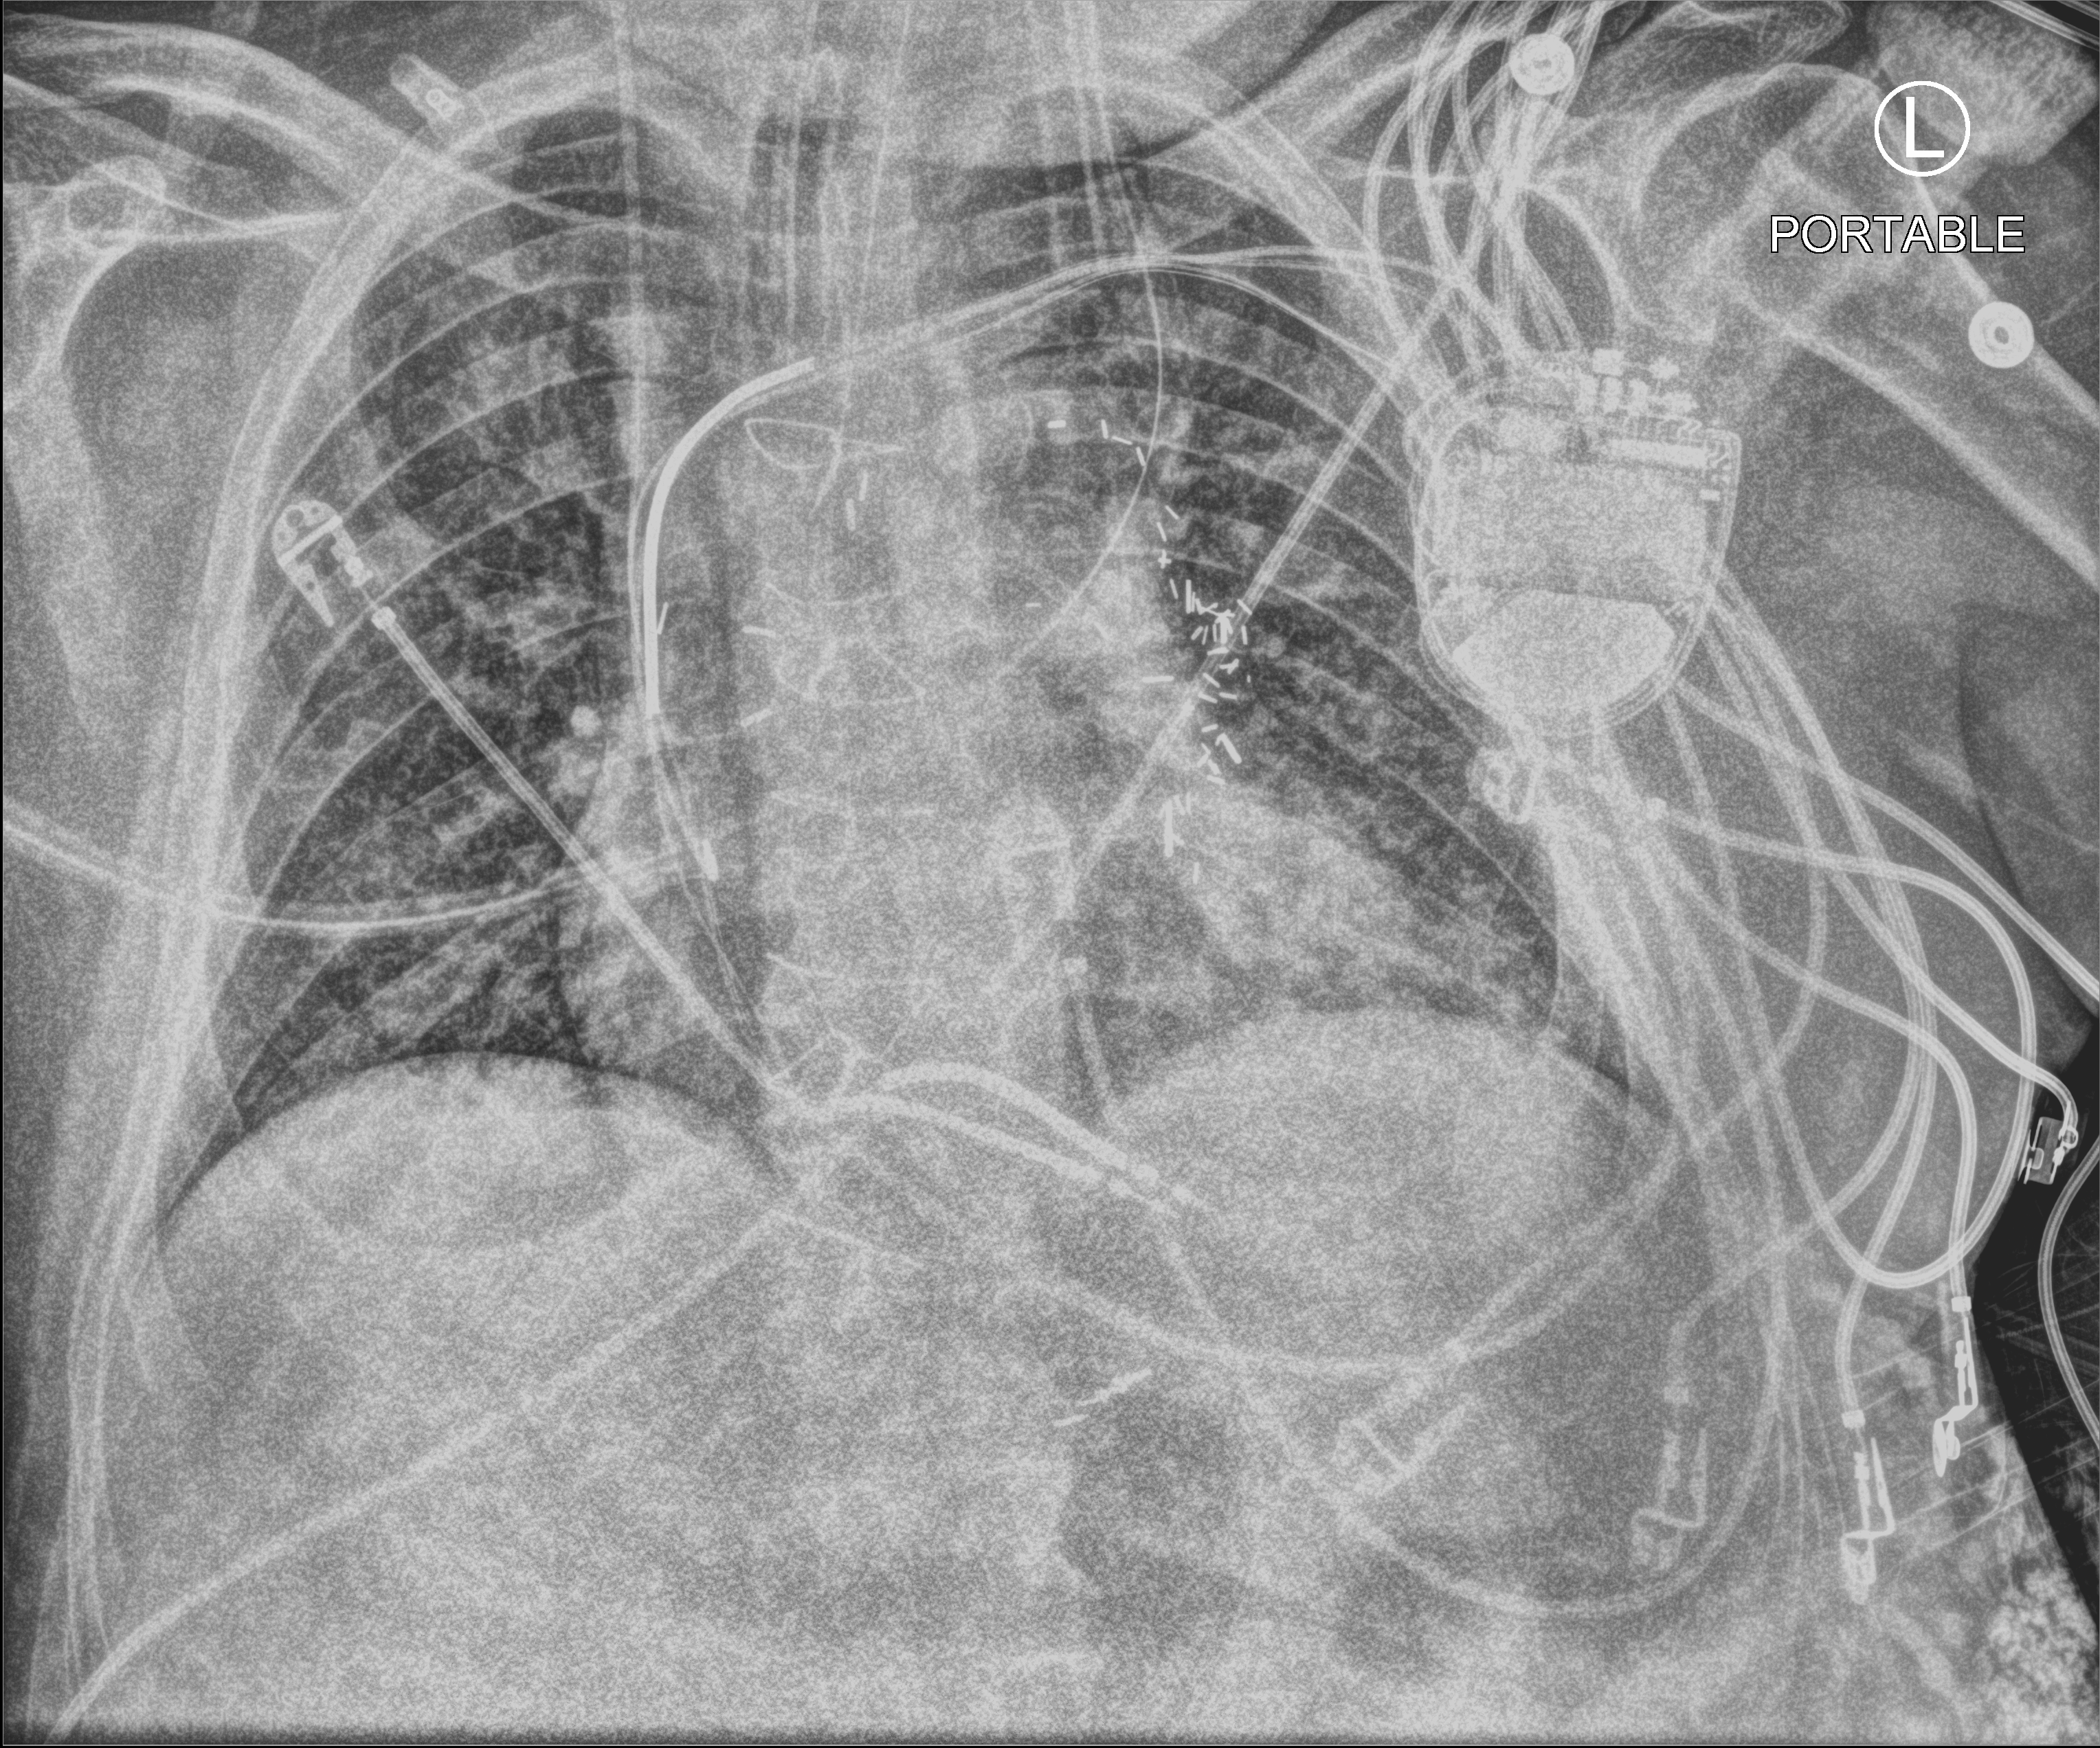
Chest X-ray (portable); anteroposterior (AP) projection. Male patient hospitalised with COVID-19, age 60–74 years.
From the hospital-stay record, not from the radiograph (when in the stay this image was taken is not recorded): mechanically ventilated during this hospital stay: yes.